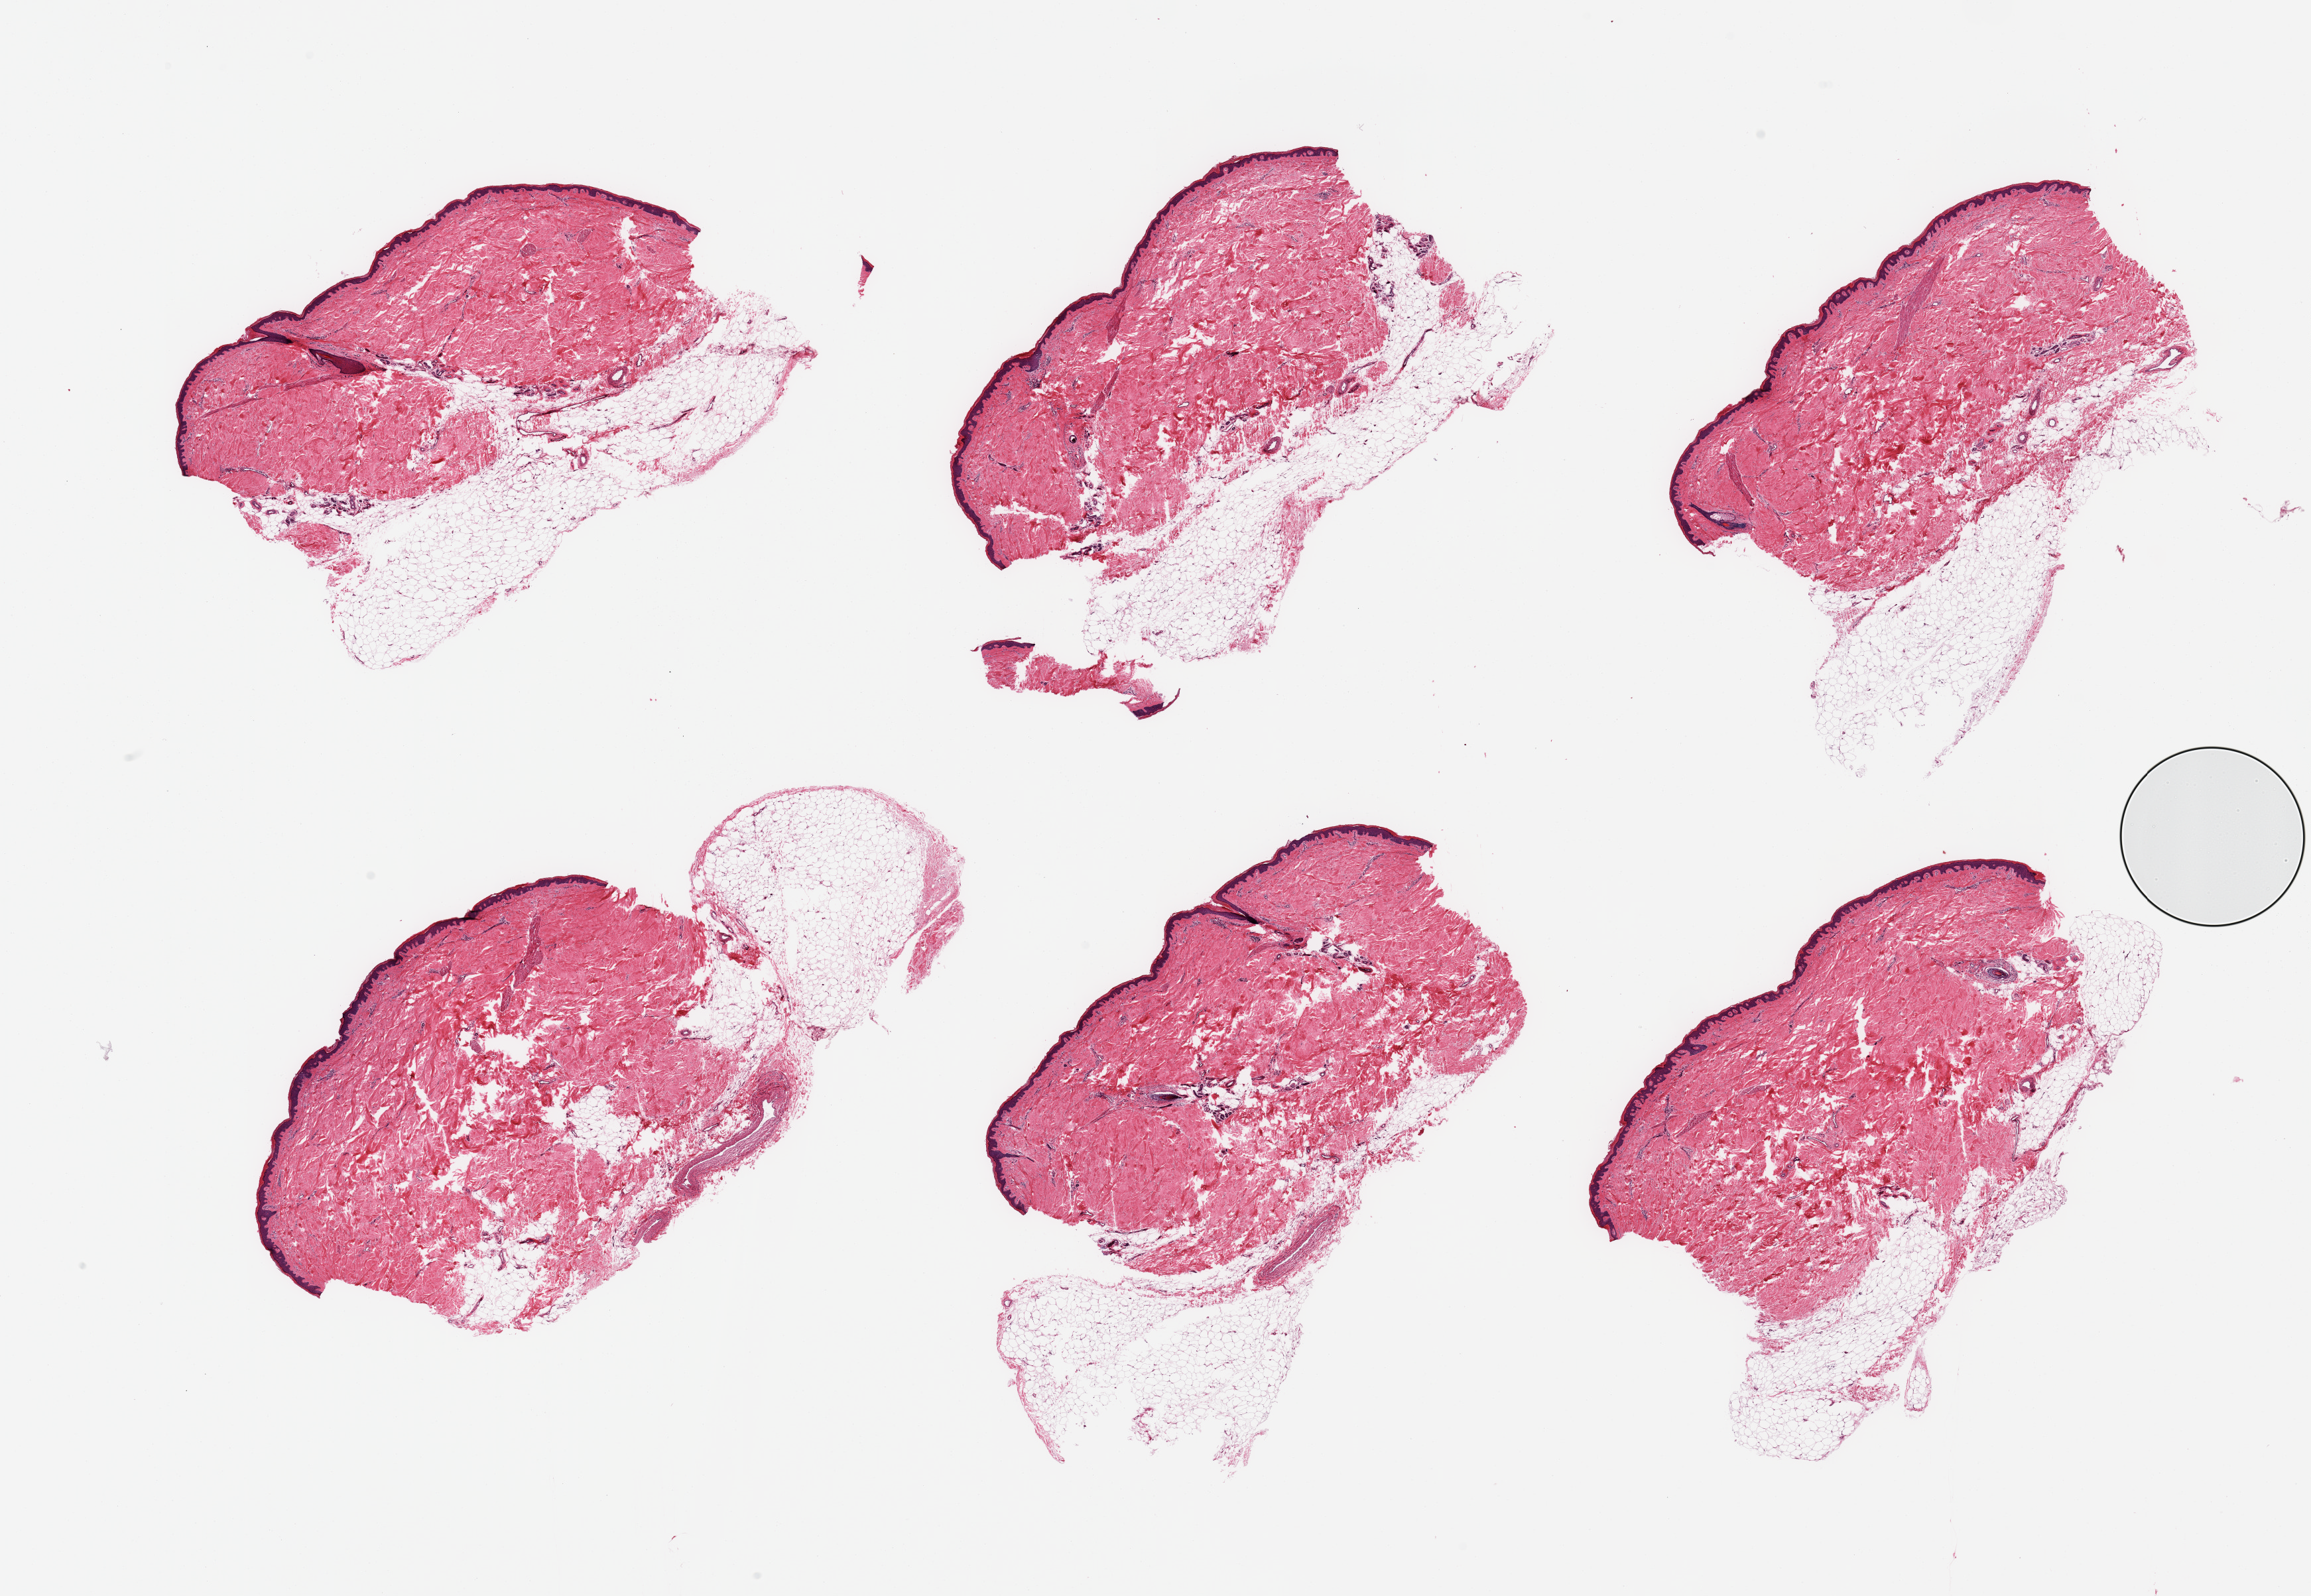
Whole-slide image, H&E stain, brightfield — shown as a low-resolution overview of the whole scanned area (about 27.6 x 19.0 mm), PAXgene-fixed, paraffin-embedded tissue, section of skin of lower leg (target tissue), tissue donor sample. Donor sex: male.
Reviewer comment on this tissue sample: 6 pieces; squamous epithelium is ~40 microns; abundant adherent dermal fat up to ~2mm.